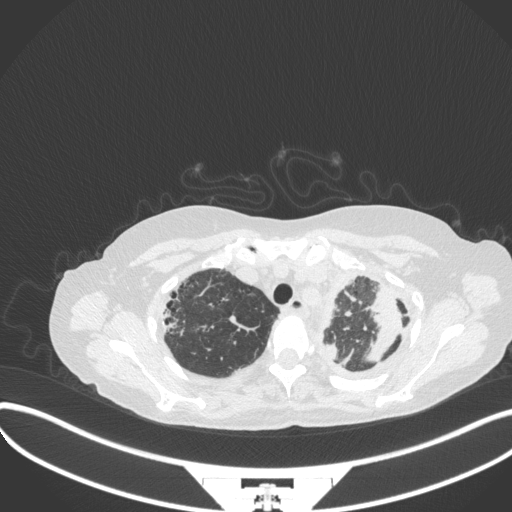
Chest CT, one axial slice; position 282 of 373 along the scan axis; reconstruction kernel B31f; 120 kVp; lung window (W 1500 / L -600 HU); 1 mm slice thickness; 512 × 512 image matrix, field of view 400 × 400 mm. Female patient, age 56 years. Case-level facts recorded for this patient, not image findings: clinical TNM (as recorded): T1 N0 M0.
Outlined on this slice (rectangle marked by the reading radiologist):
- lung tumour (recorded histology: adenocarcinoma): bounding box <365,278,401,367> (left, top, right, bottom; pixels)